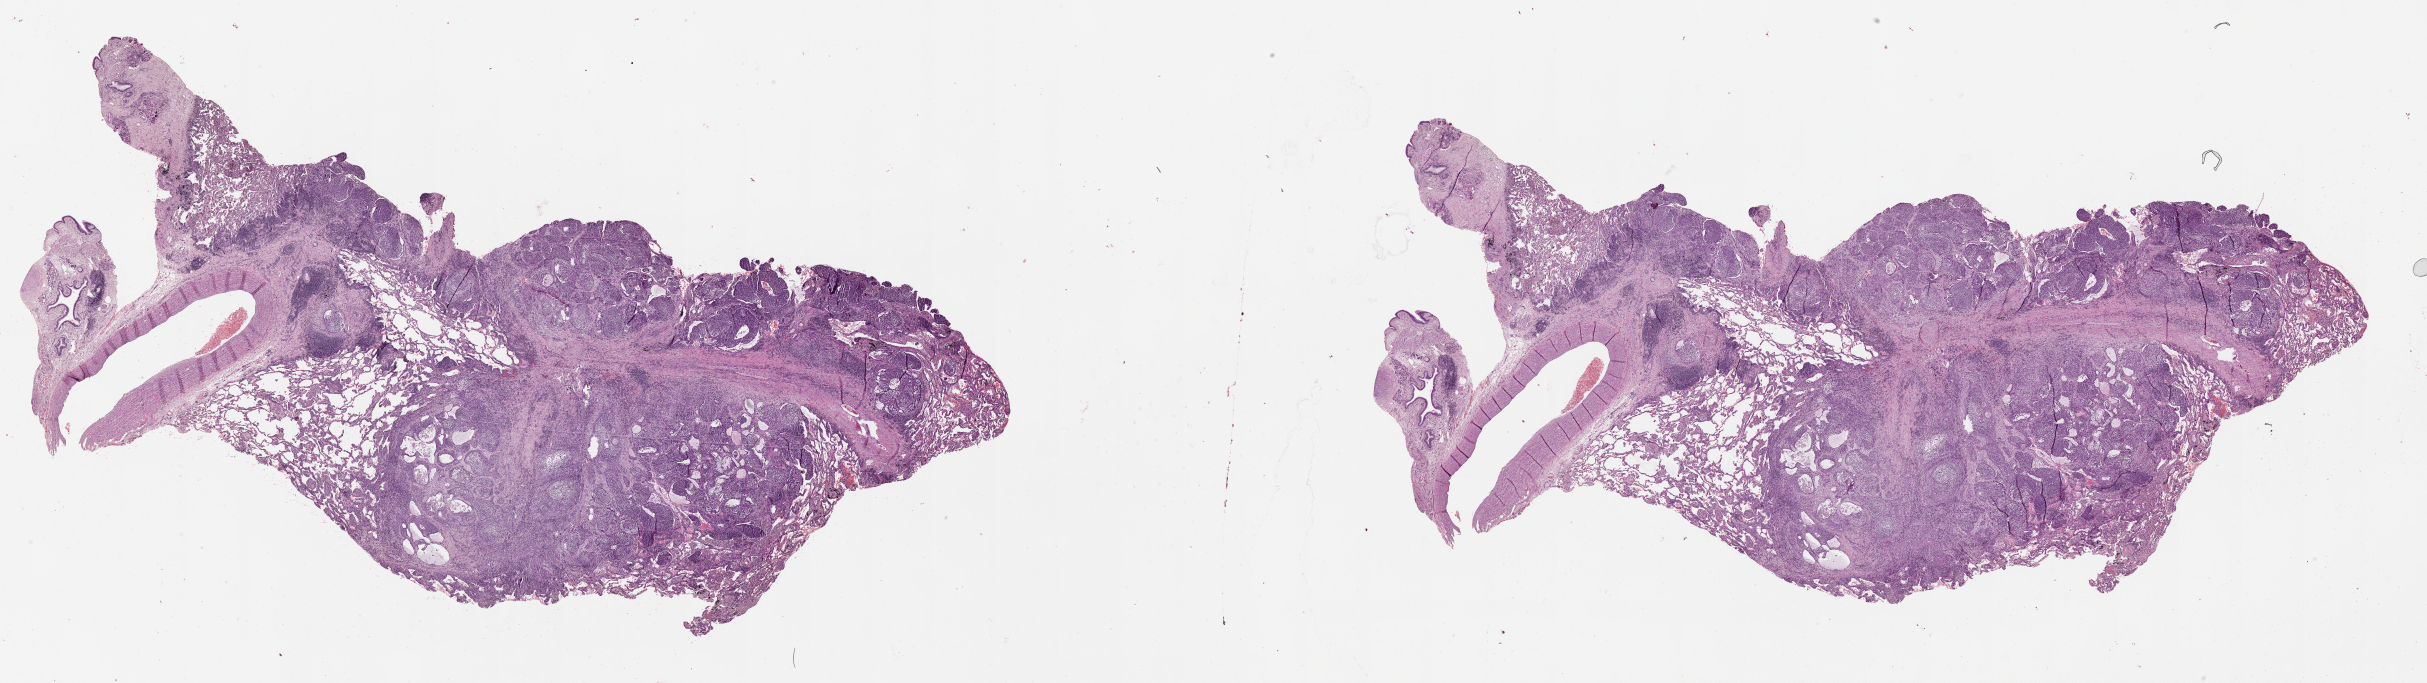
Digitized H&E-stained tissue section (whole slide) — whole scanned area (about 39.1 x 11.0 mm, slide scanned at 20x) shown as a low-resolution overview. Tumour tissue sample, lung. Patient: female, age 63 years.
Patient diagnosis (cohort enrolment): squamous cell carcinoma (lung).